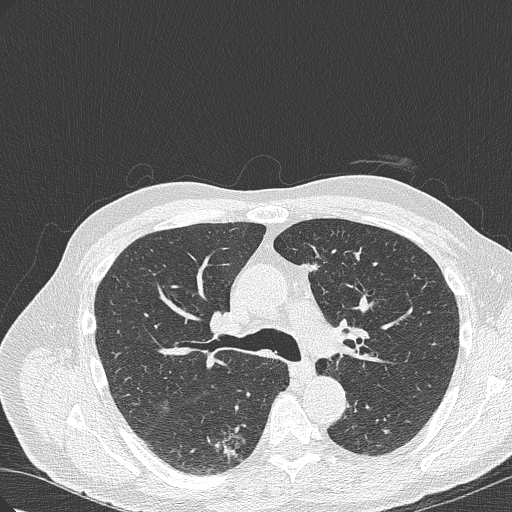
Chest CT (low-dose screening protocol), one axial image. Baseline screening round. Lung window (W 1500 / L -600 HU). Slice 112 of 322 in the series. 512 × 512 image matrix, field of view 350 × 350 mm. Male, age 70 years at enrolment.
Lesion marked by an expert reader, bounding box (x1, y1, x2, y2) in pixels: (201, 419, 265, 467). The screening reader recorded 4 non-calcified nodules or masses ≥4 mm on this exam (right lower lobe, right lower lobe, right upper lobe, right lower lobe); which of them this box marks is not recorded. Official screen result: positive, change unspecified: nodule(s) >= 4 mm or enlarging nodule(s), mass(es), or other non-specific abnormalities suspicious for lung cancer. Later outcome: lung cancer diagnosed 978 days after this screen (after the third annual screen) — bronchiolo-alveolar adenocarcinoma, NOS, right lower lobe, poorly differentiated (G3), stage IB (AJCC 6th edition), 30 mm at pathology.